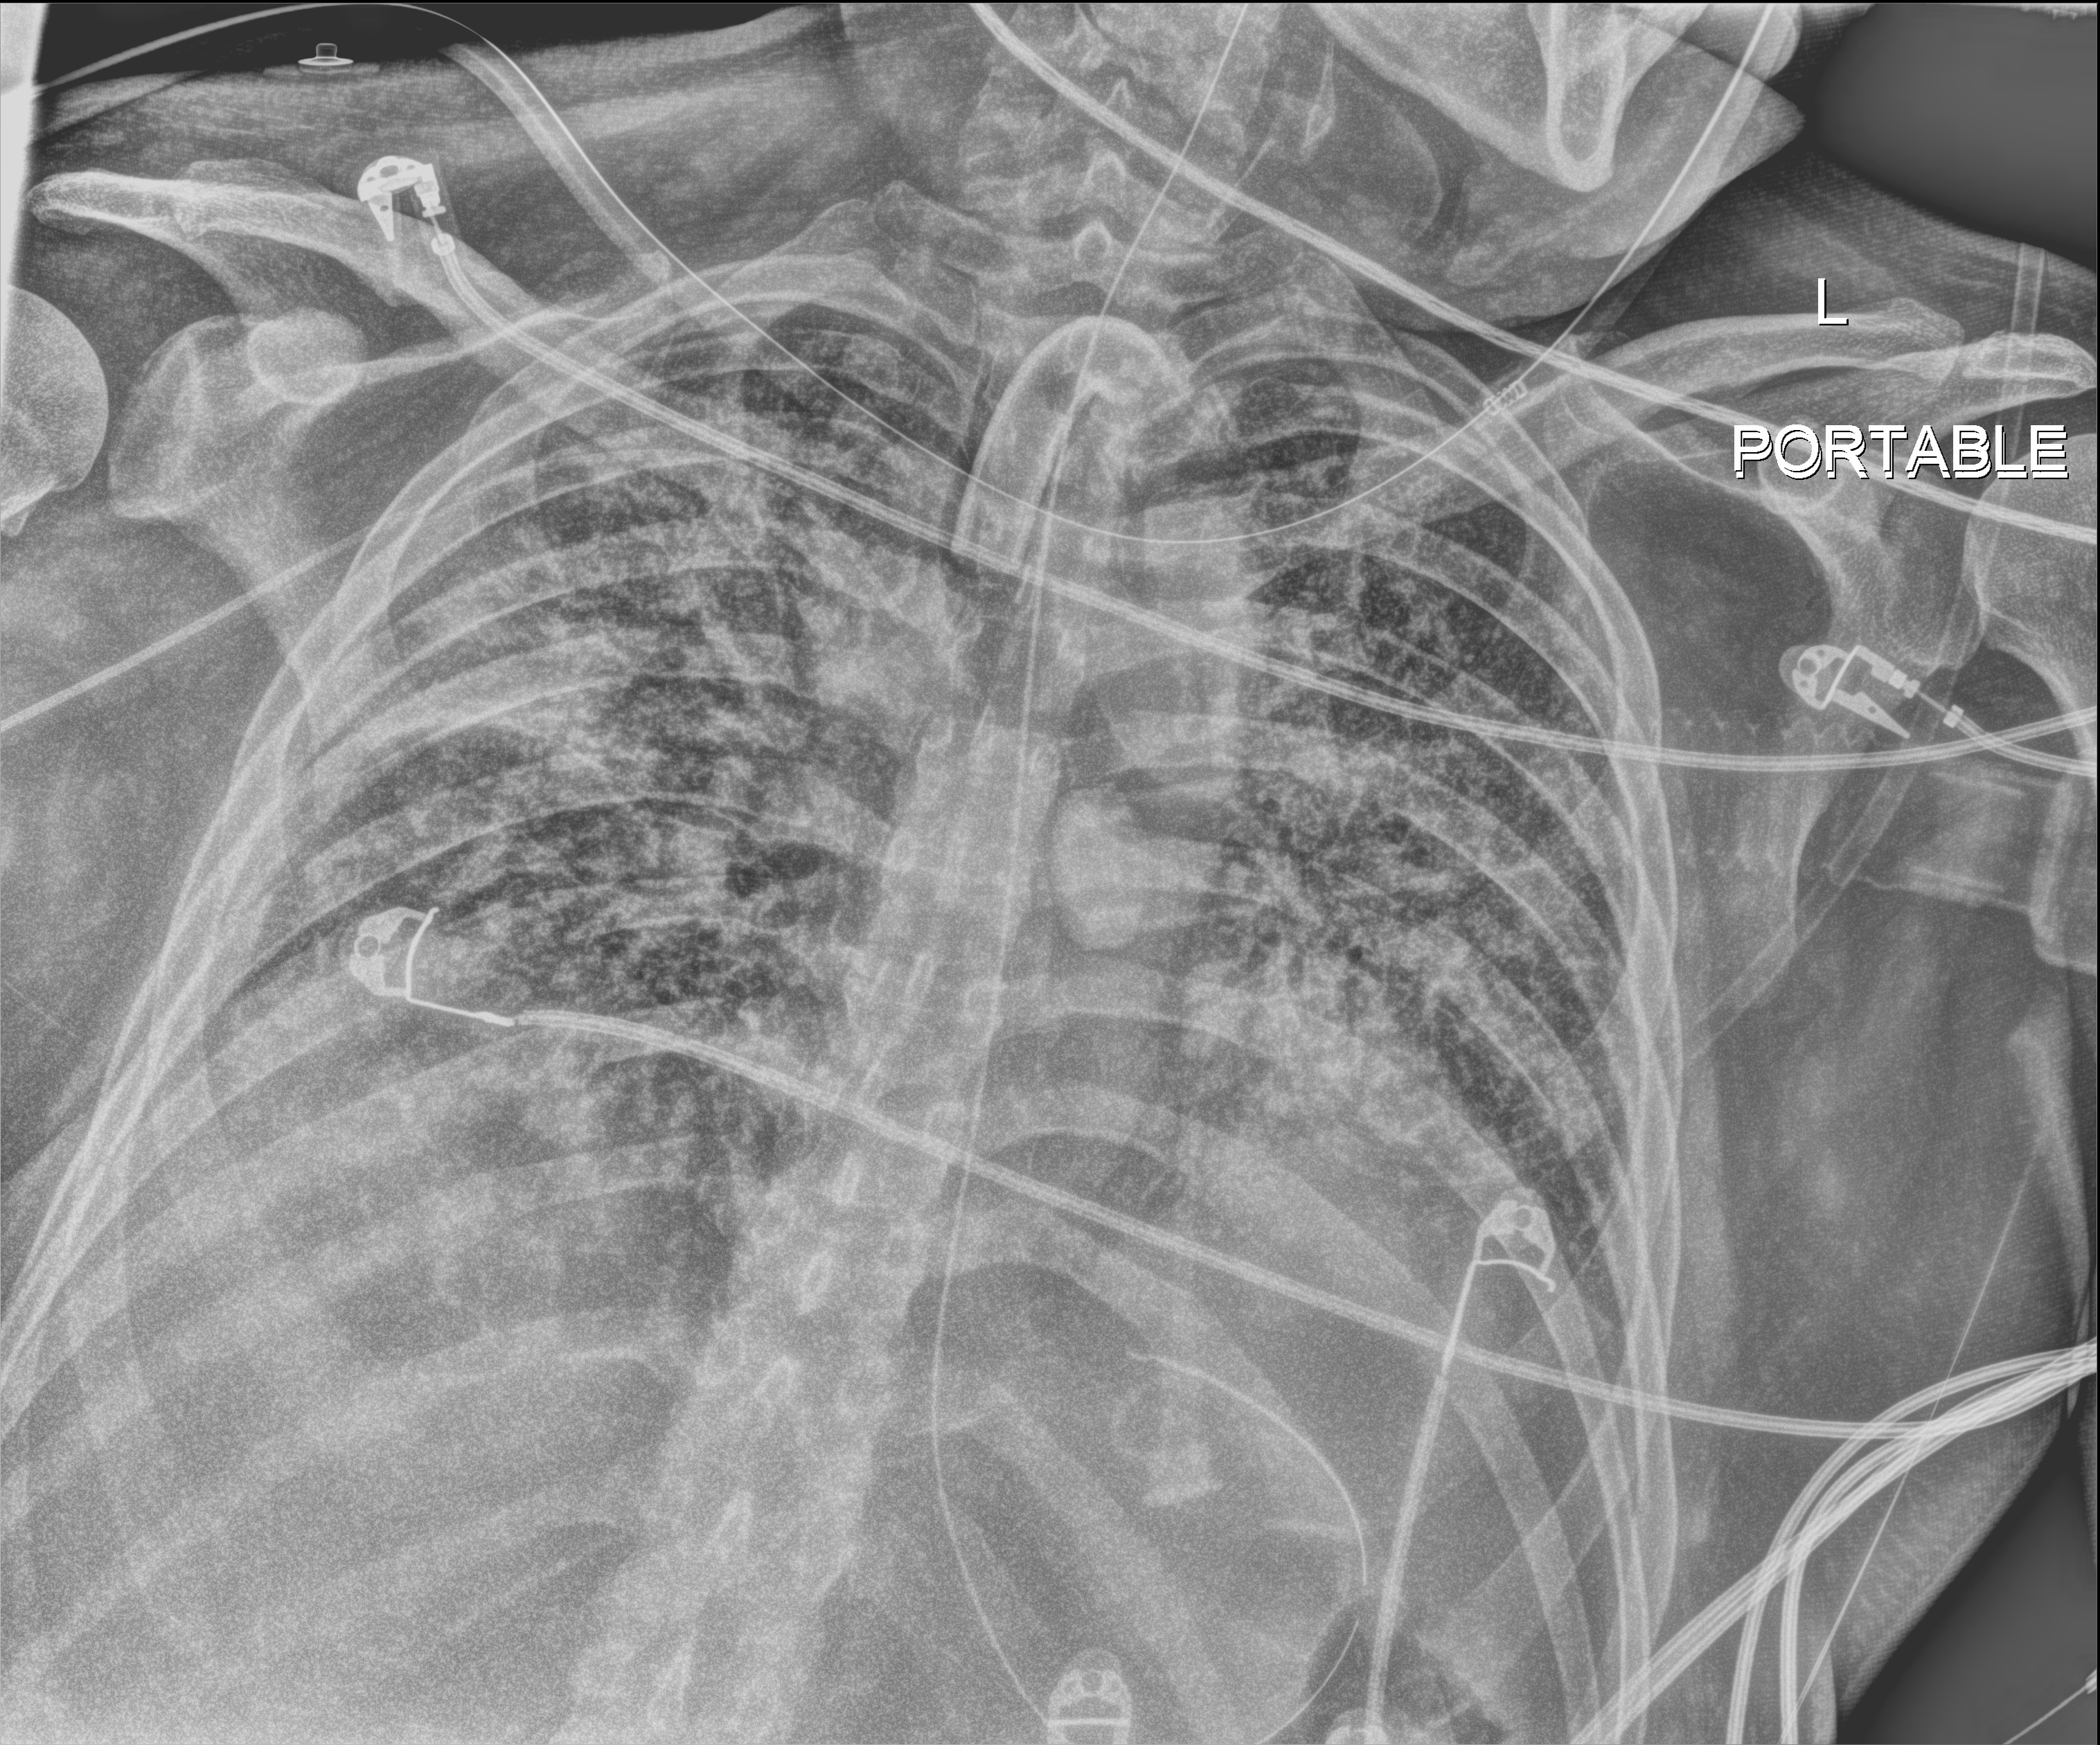
Portable chest radiograph; anteroposterior (AP) projection. Patient hospitalised with COVID-19; male, aged 18–59 years.
From the hospital-stay record, not from the radiograph (when in the stay this image was taken is not recorded): admitted to intensive care during this hospital stay: yes; mechanically ventilated during this hospital stay: yes.